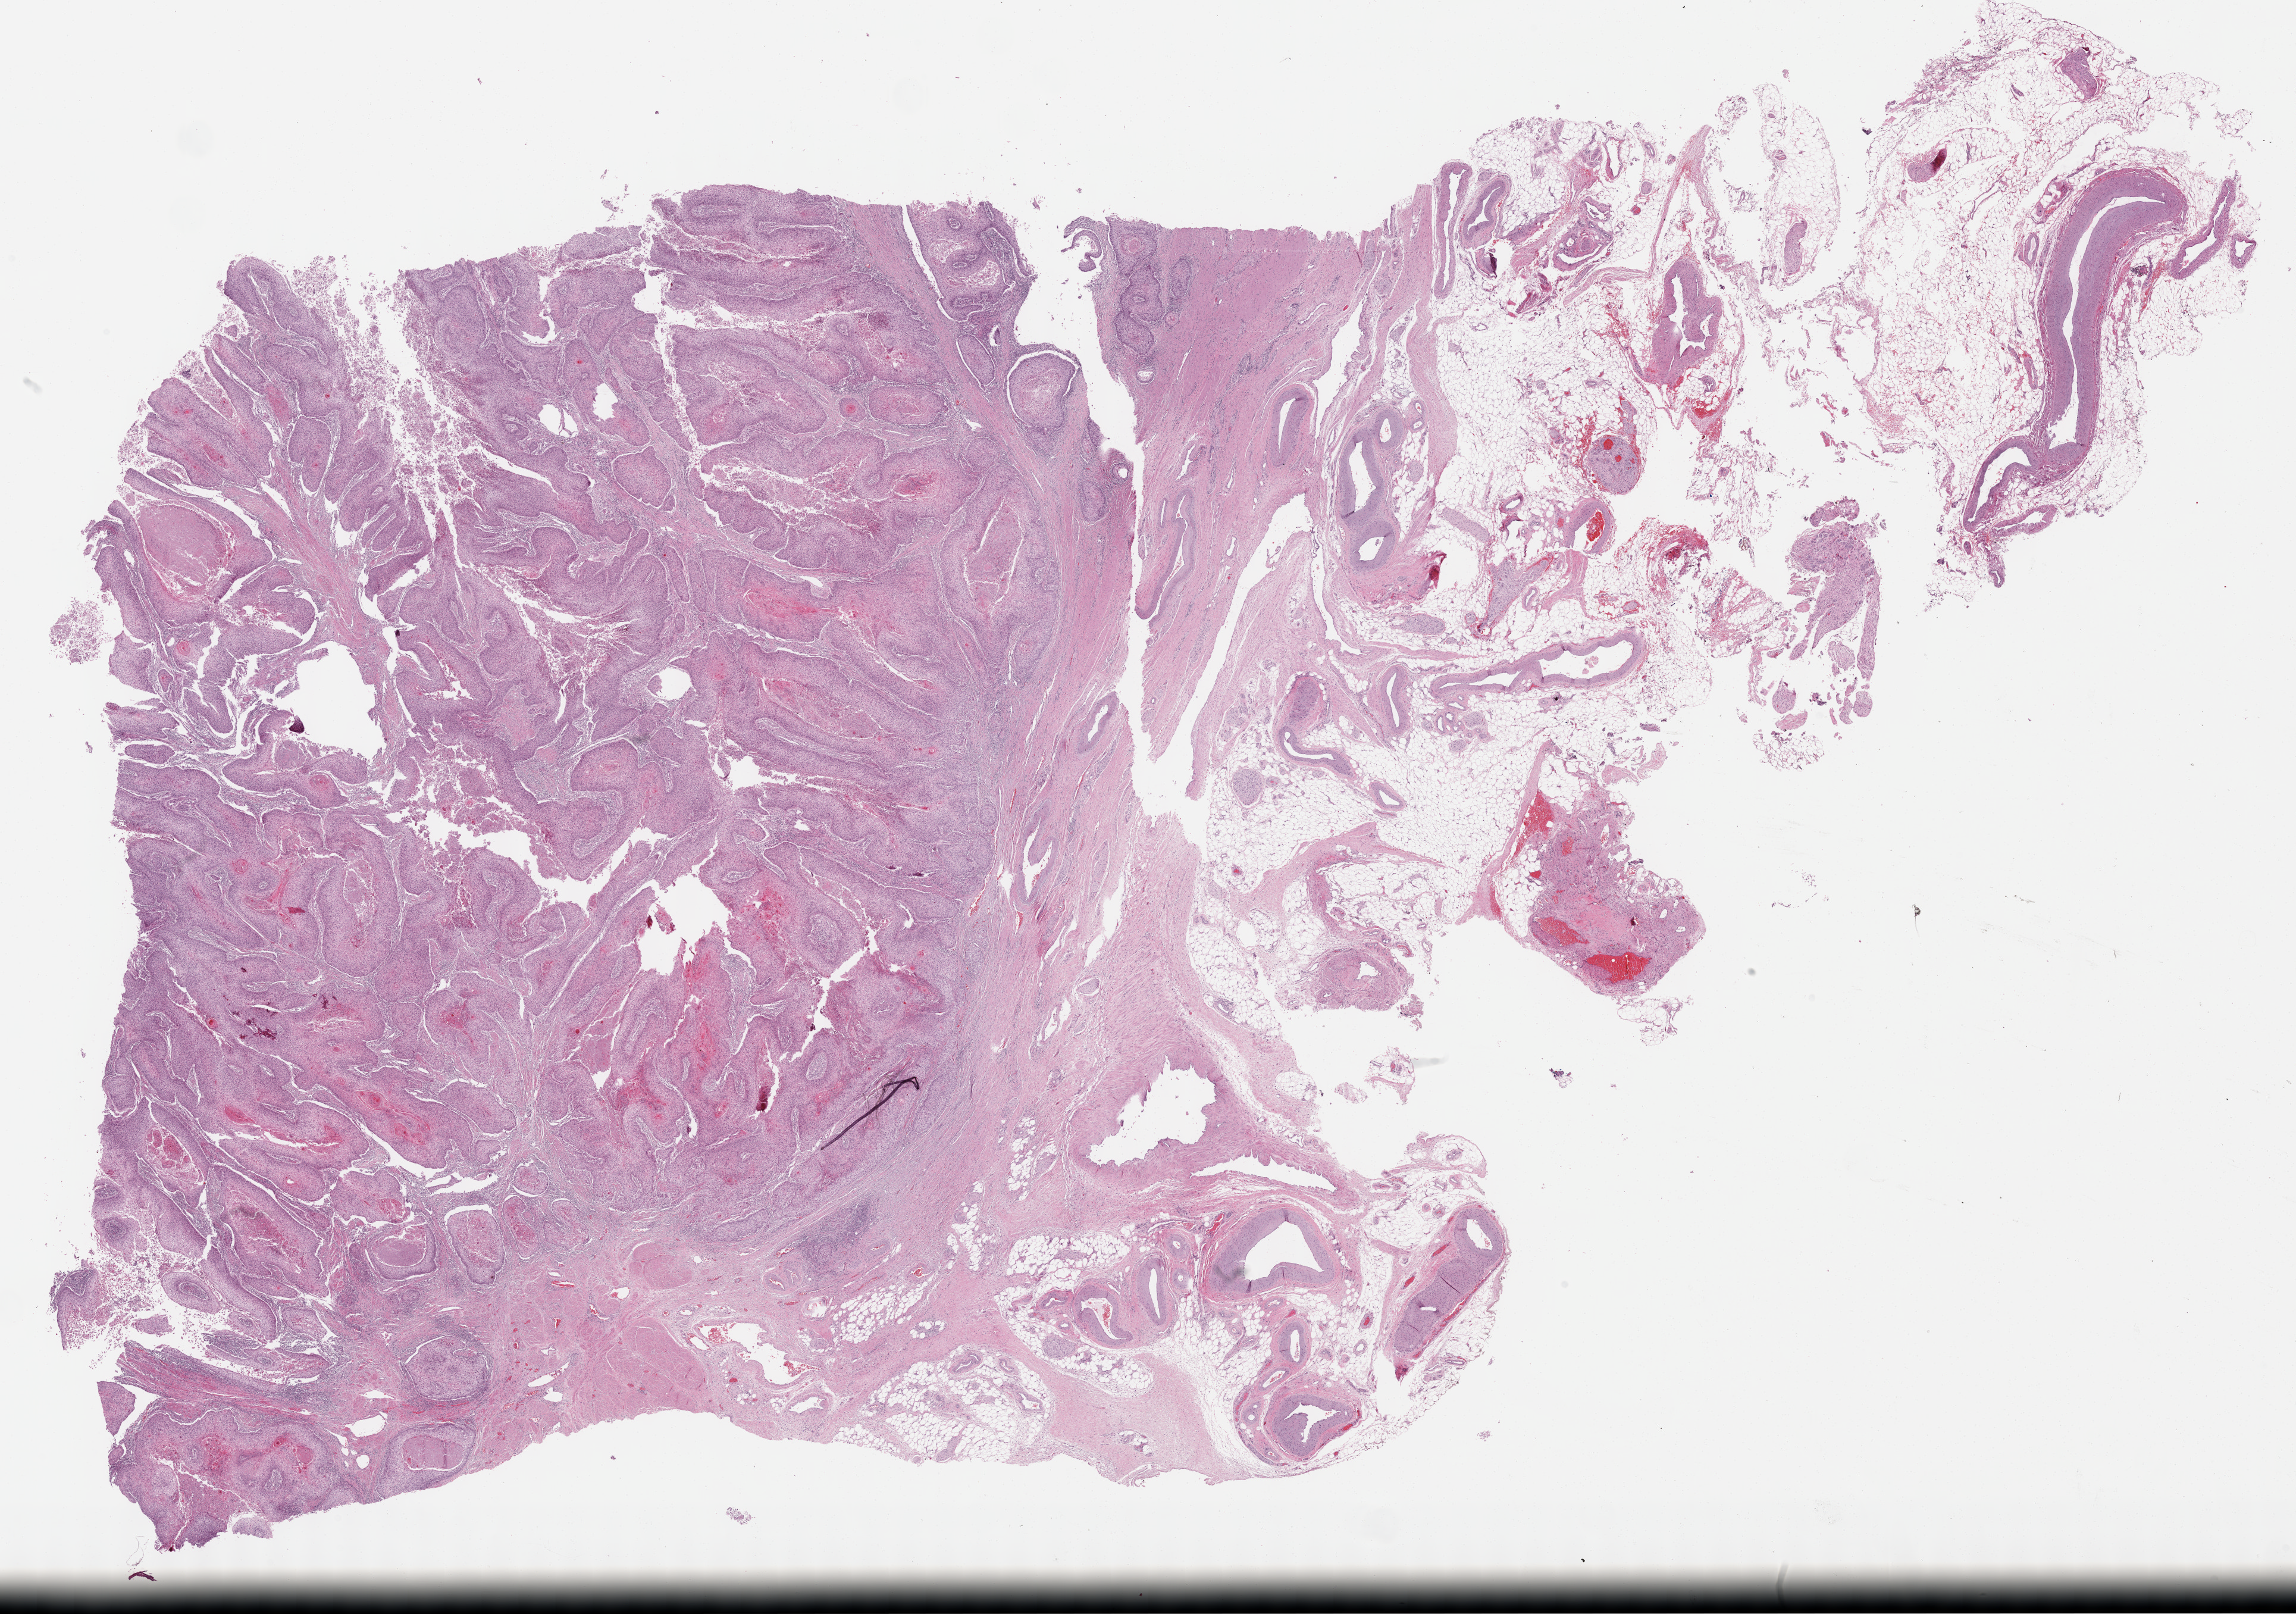
Hematoxylin and eosin (H&E) stained whole-slide image — whole scanned area (about 31.2 x 21.9 mm) shown as a low-resolution overview; formalin-fixed paraffin-embedded (FFPE) diagnostic section; sample: primary tumour, bladder. Male, age 65 years at initial diagnosis. Histologic grade: high grade.
* TNM: T3 N0 M0
* lymph nodes positive (case pathology): 0 of 46 examined
* AJCC pathologic stage: III
* diagnosis: Transitional cell carcinoma